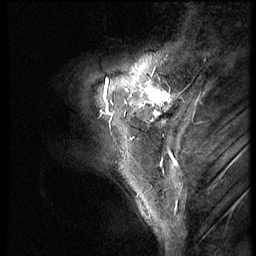
Breast MRI (dynamic contrast-enhanced), one sagittal slice; slice 13 of 56 in the series (ordered by position); 3 images stored at this slice position (order not interpretable as contrast timing); 1.5 T; TE 4.2 ms, TR 9 ms; 2.5 mm slice thickness; 256 × 256 image matrix. Female patient, age 46 years. Case-level facts recorded for this patient, not image findings: setting: breast cancer imaged before/during neoadjuvant chemotherapy; receptor status: HER2-positive.
Outlined on this slice (semi-automatic segmentation, software-assisted and operator-edited):
- analysis volume of interest (the breast-tissue region the enhancement analysis was run in; not a lesion): bounding box (x1, y1, x2, y2) in pixels: (79, 68, 190, 143)
- tumour enhancement mask (voxels above the 140 % enhancement threshold inside the analysis volume of interest): (104, 79, 167, 115)